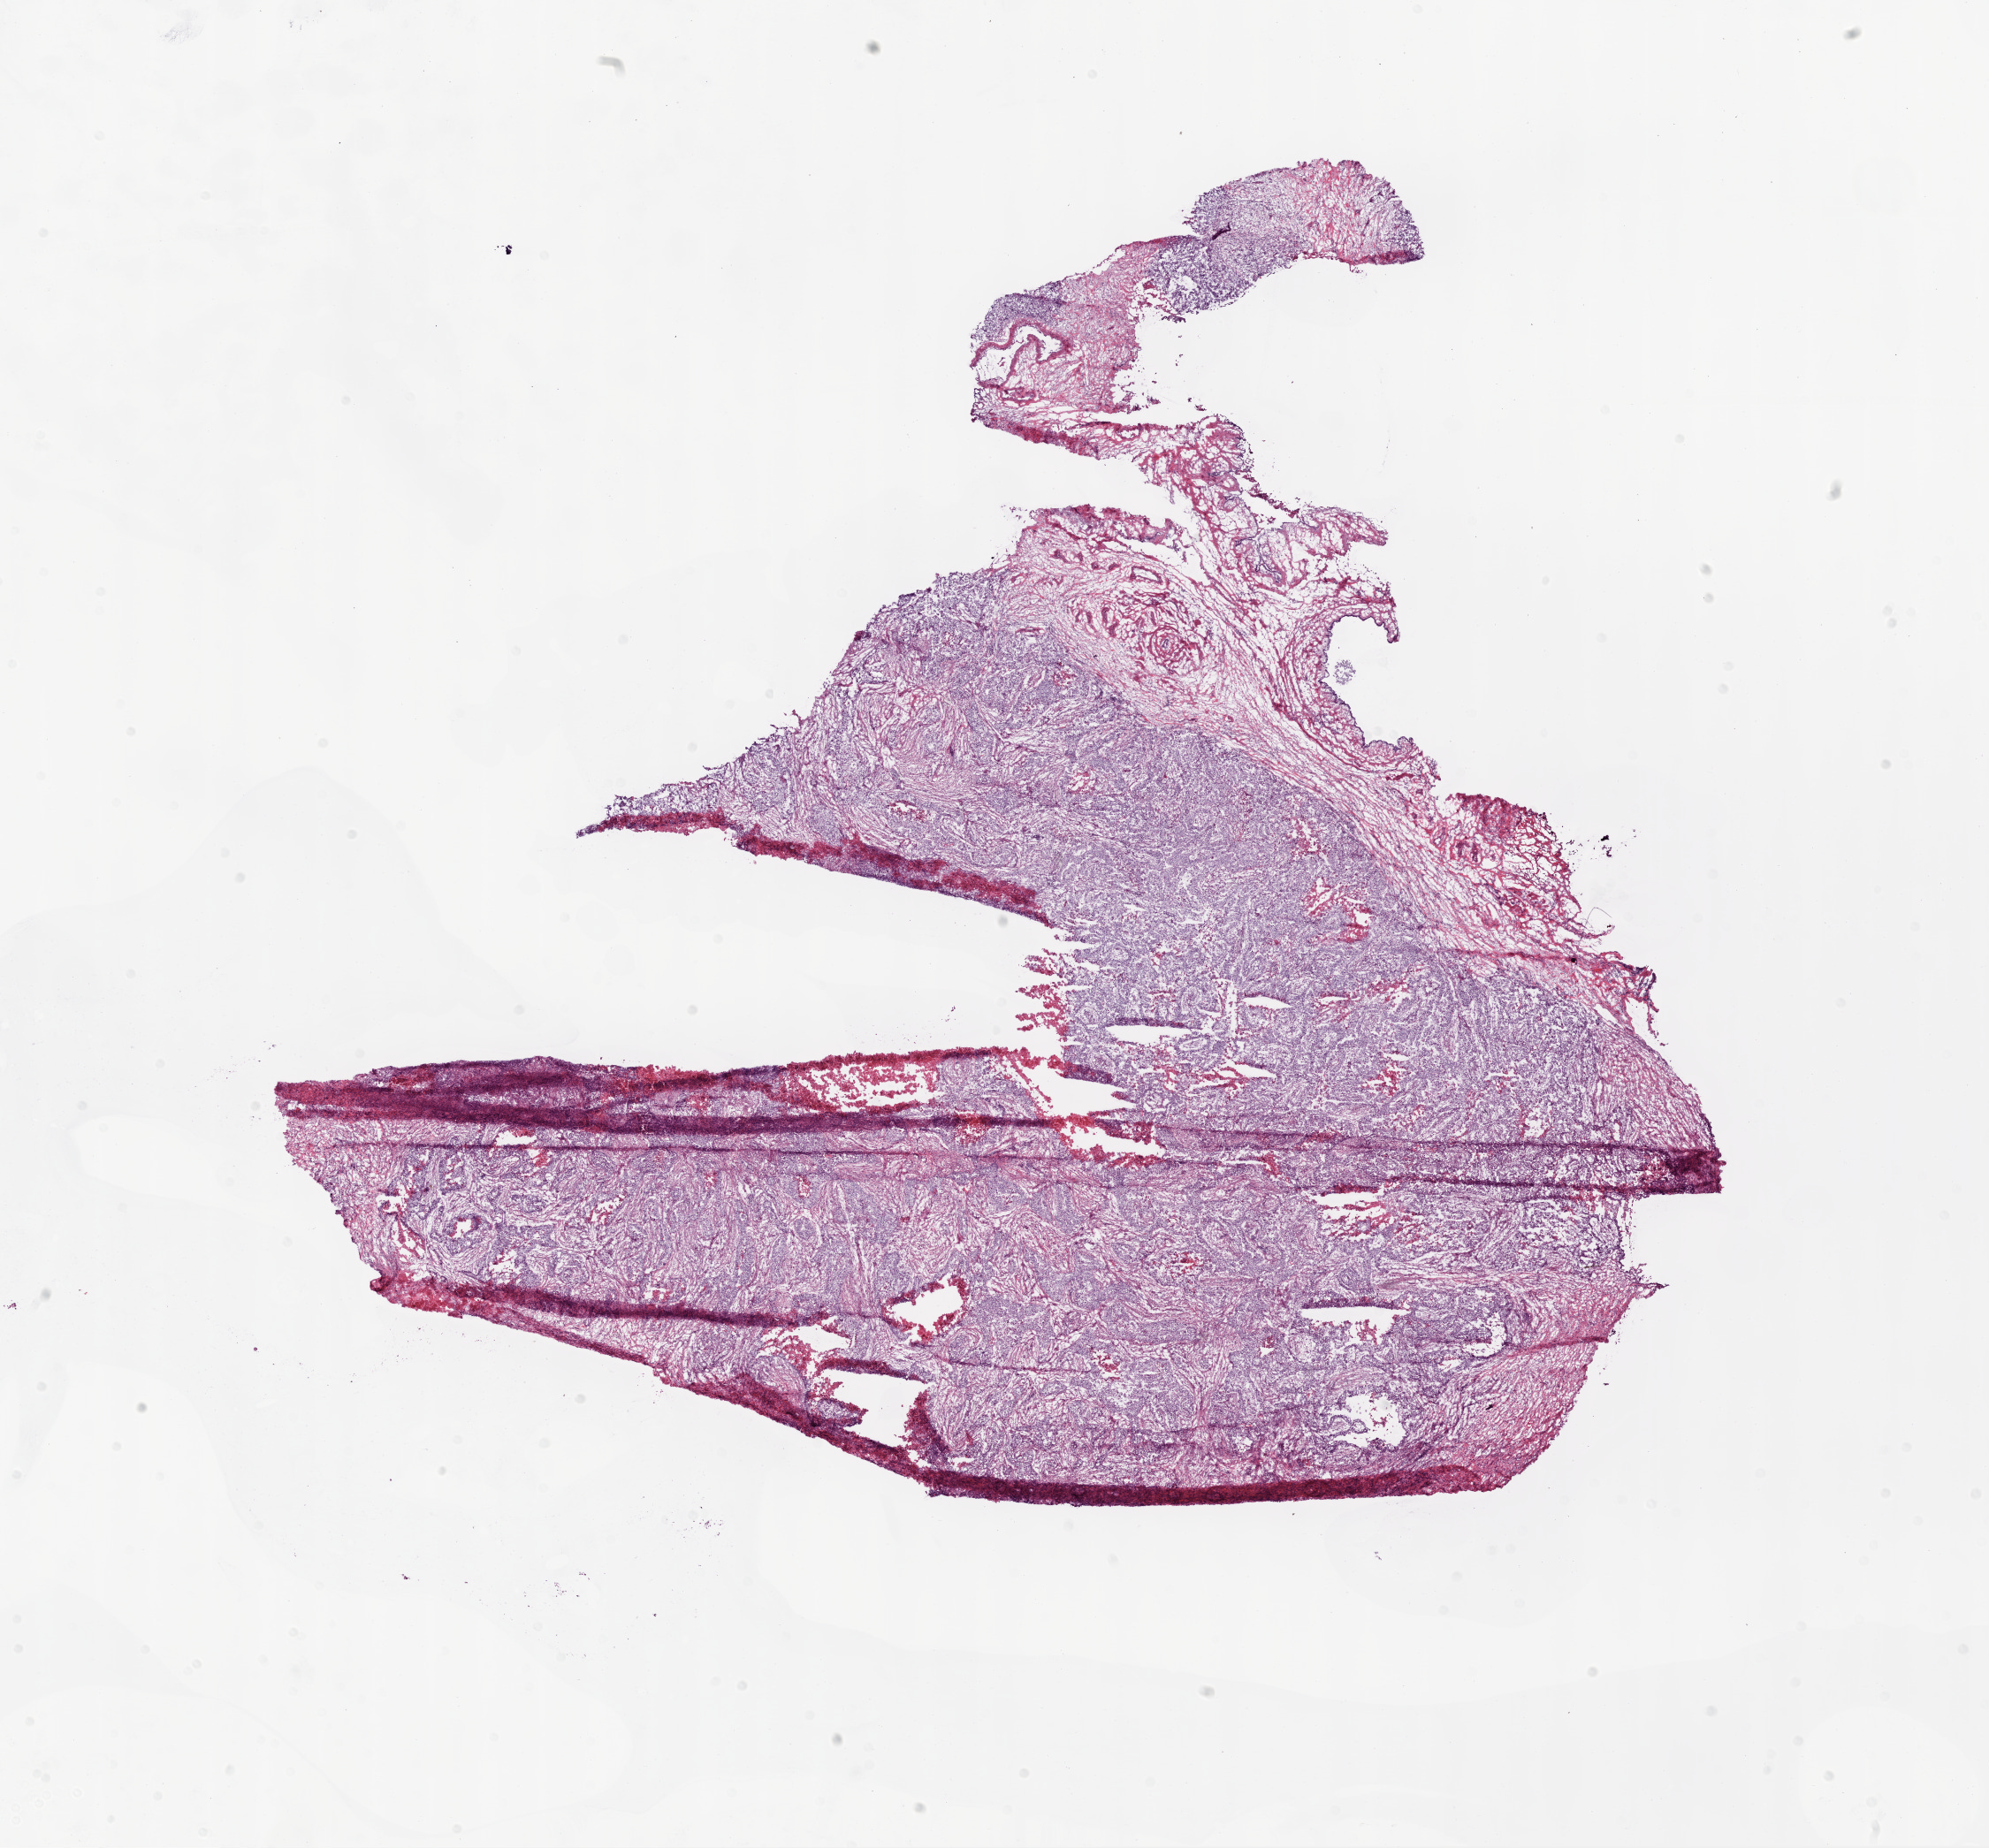
Digitized H&E tissue section (whole slide) — whole scanned area (about 18.1 x 16.8 mm, from a 20x scan) shown as a low-resolution overview; frozen section; sample: primary tumour, ovary. Female, age 72 years at initial diagnosis. Histologic grade: G3 (poorly differentiated). Composition of this section per pathologist review: tumour cells 85%, tumour nuclei 95%, normal cells 0%, stromal cells 10%, necrosis 5%.
FIGO stage: IIIC. Histologic diagnosis: Serous cystadenocarcinoma, NOS.